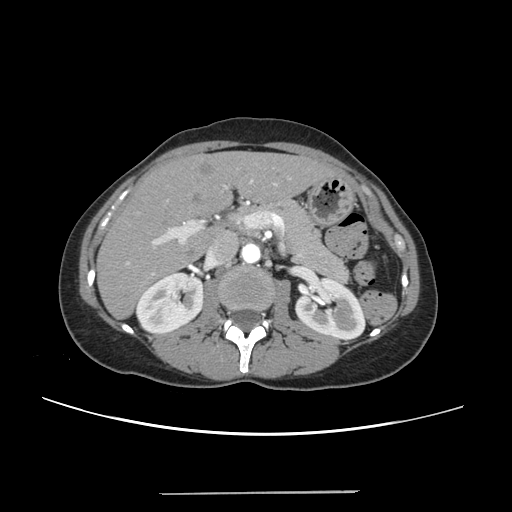
Contrast-enhanced abdominal CT, one axial slice. Slice 127 of 240 in the series (ordered by position). Intravenous contrast given. Soft-tissue window (W 400 / L 40 HU). 512 × 512 image matrix, field of view 371 × 371 mm. Female patient, age 60 years. Case-level facts recorded for this patient, not image findings: diagnosis: colorectal cancer liver metastases, imaged before liver resection; multiple liver metastases: no; largest metastasis: 1.5 cm.
Outlined on this slice (manually delineated by an expert):
- liver: box from (x=99, y=152) to (x=332, y=317) px
- planned liver remnant (the part of the liver to remain after resection): (x=99, y=153)–(x=331, y=317)
- portal vein (with intrahepatic branches): (x=126, y=178)–(x=290, y=275)
- liver metastasis: (x=200, y=163)–(x=214, y=176)